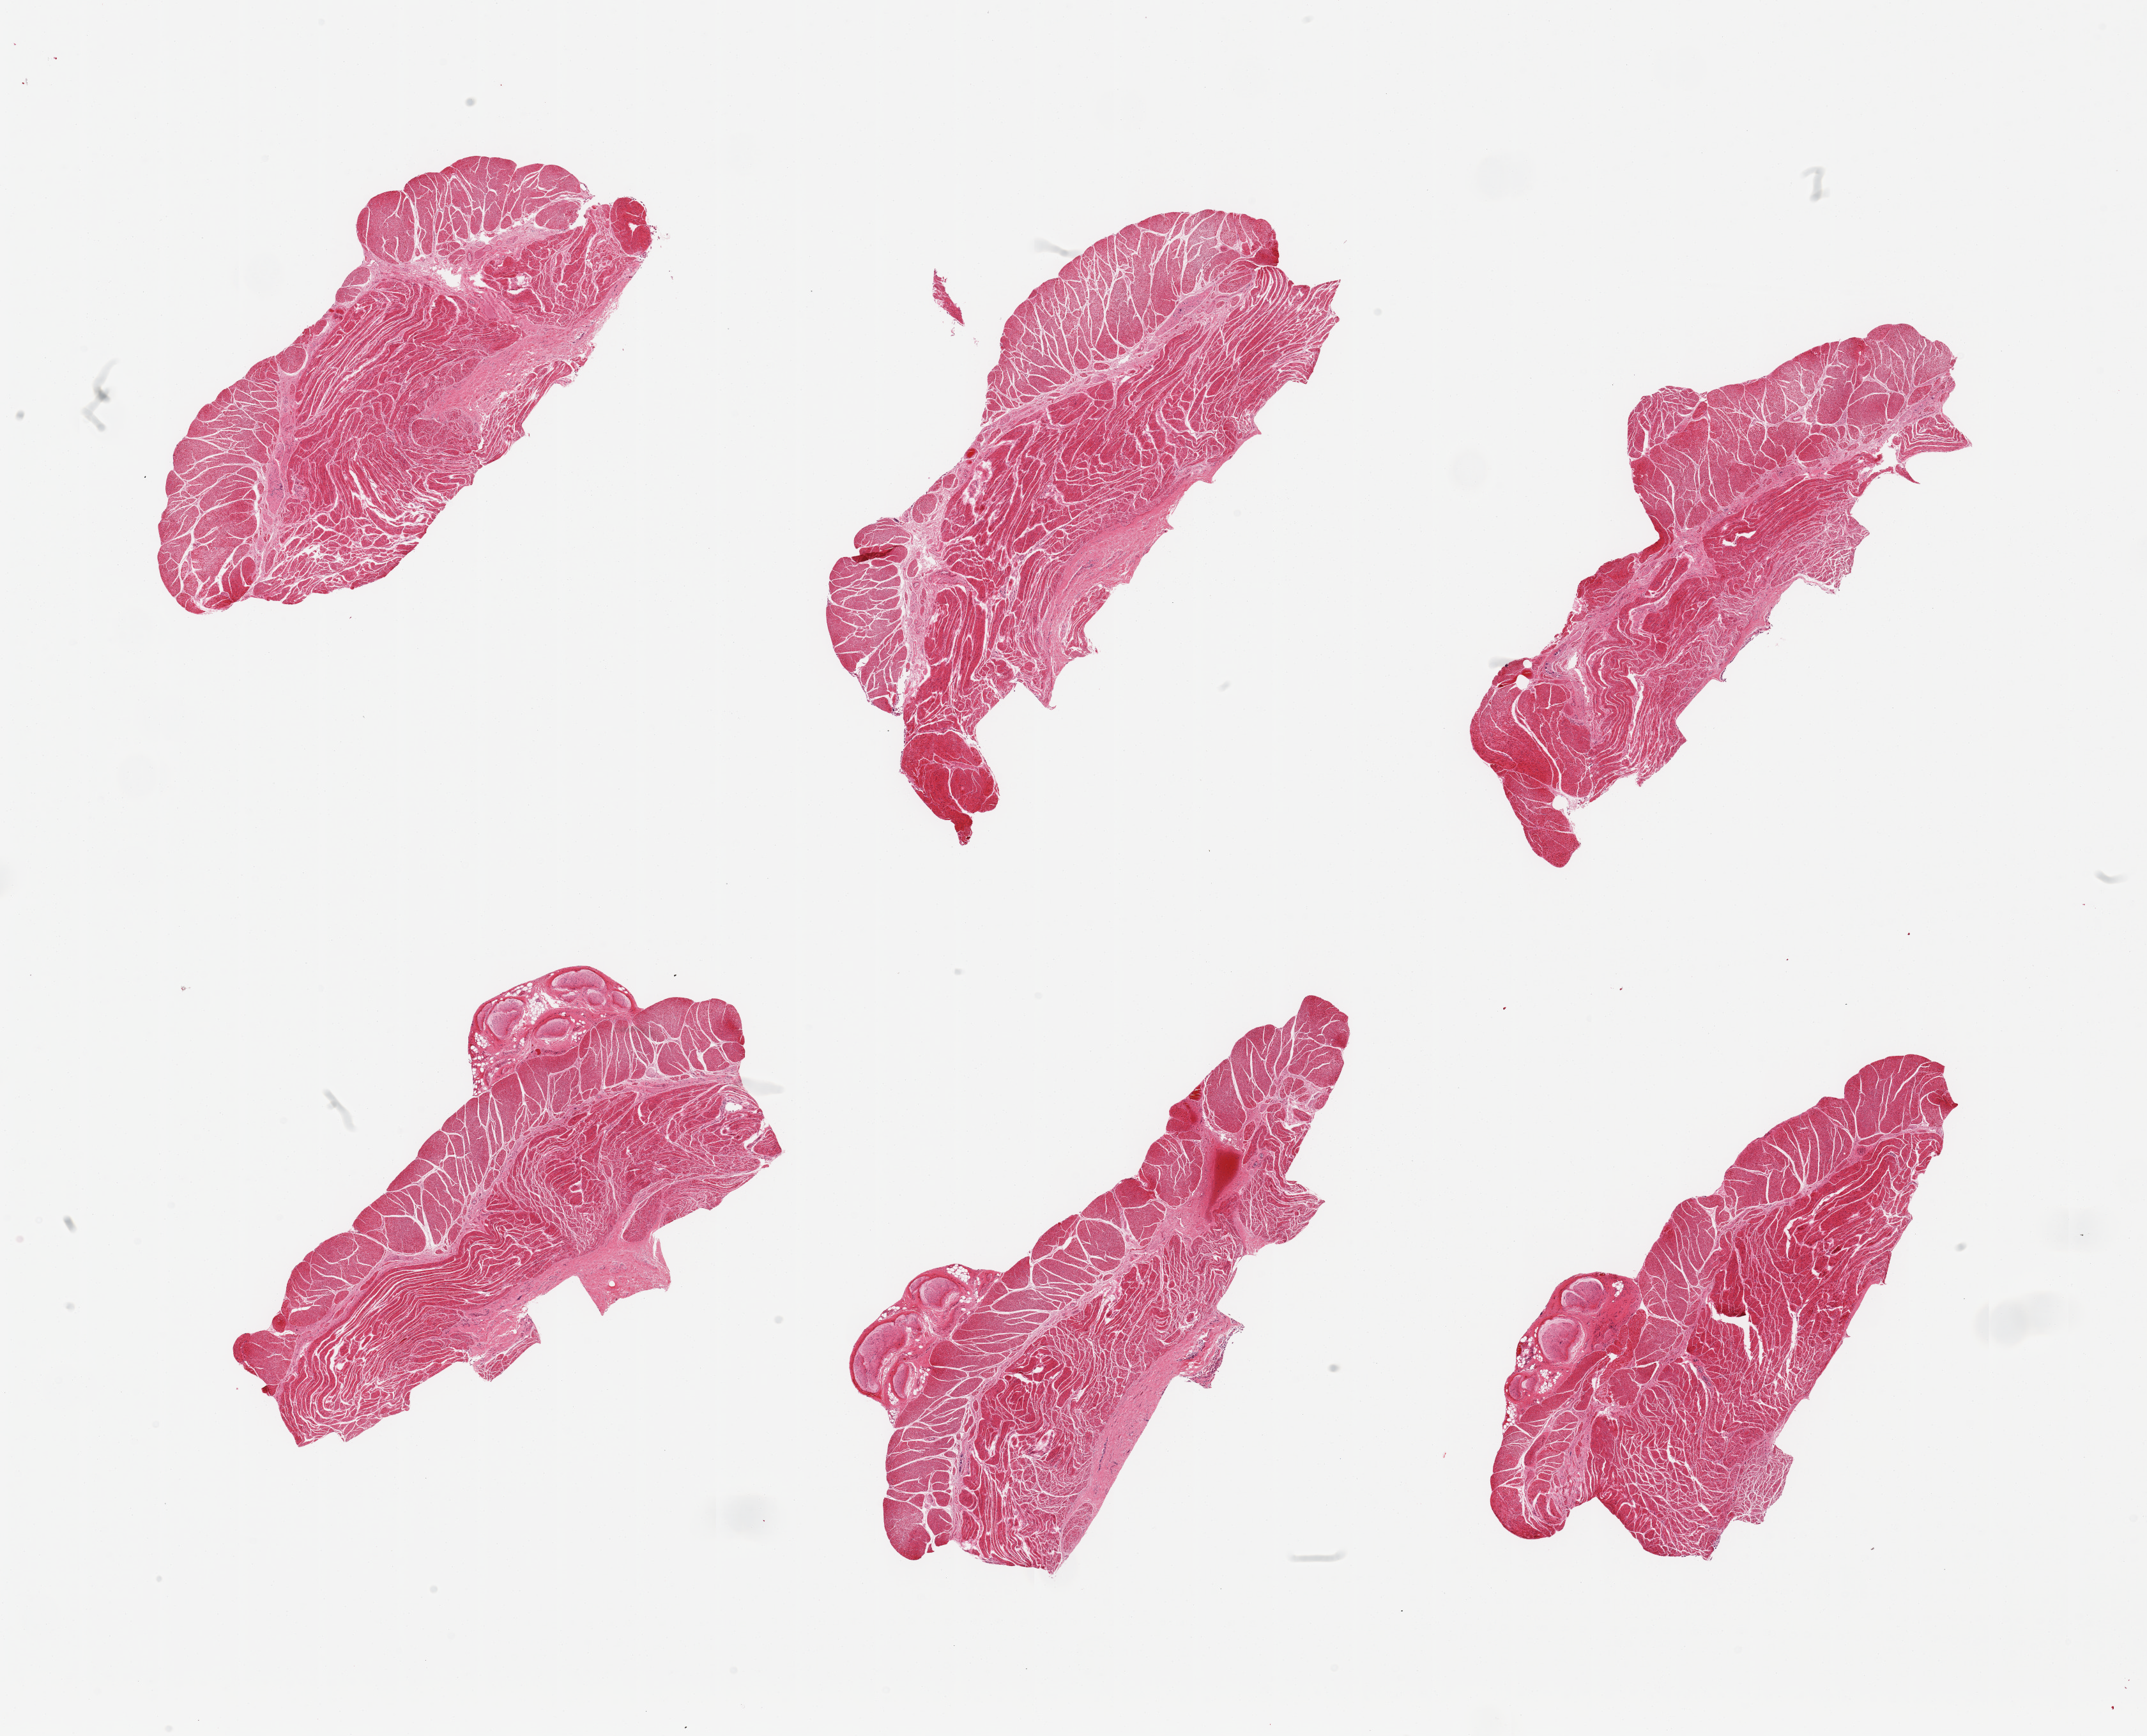
Digitized hematoxylin and eosin (H&E)-stained section, brightfield — whole scanned area (about 26.6 x 21.5 mm) shown as a low-resolution overview, PAXgene-fixed paraffin-embedded (PFPE) section, section of esophageal muscle (target tissue), tissue donor sample. Donor: male.
Pathologist's review note for this sample: 6 pieces; target muscularis, few with small attachment of fat/nerve.